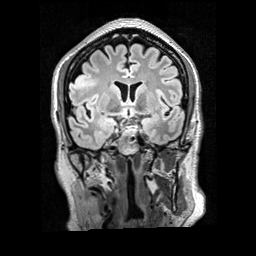
Brain MRI from a brain-tumour surgery series, one coronal slice. Slice 116 of 200 in the series (ordered by position). T2 FLAIR. 1 mm slice thickness. 256 × 256 image matrix, field of view 256 × 256 mm. Case-level facts recorded for this patient, not image findings: histopathology: Glioblastoma; WHO grade: 4; IDH mutation: no.
Annotated regions visible in this slice (expert manual segmentation):
- tumour: box from (x=70, y=72) to (x=97, y=90) px